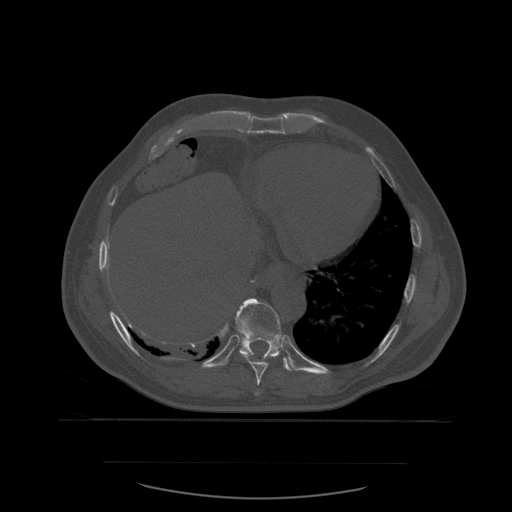
CT including the spine, one axial slice. Slice 330 of 590 in the series (ordered by position). Bone window (W 1800 / L 400 HU). 512 × 512 image matrix, field of view 479 × 479 mm. Patient age 71 years. From the clinical record (not read from this slice): primary cancer: lung.
Annotated regions visible in this slice (semi-automatic segmentation, software-assisted and operator-edited):
- T10 vertebra: bounding box [x1, y1, x2, y2] px = [235, 299, 293, 372]
- T9 vertebra: [245, 356, 278, 396]